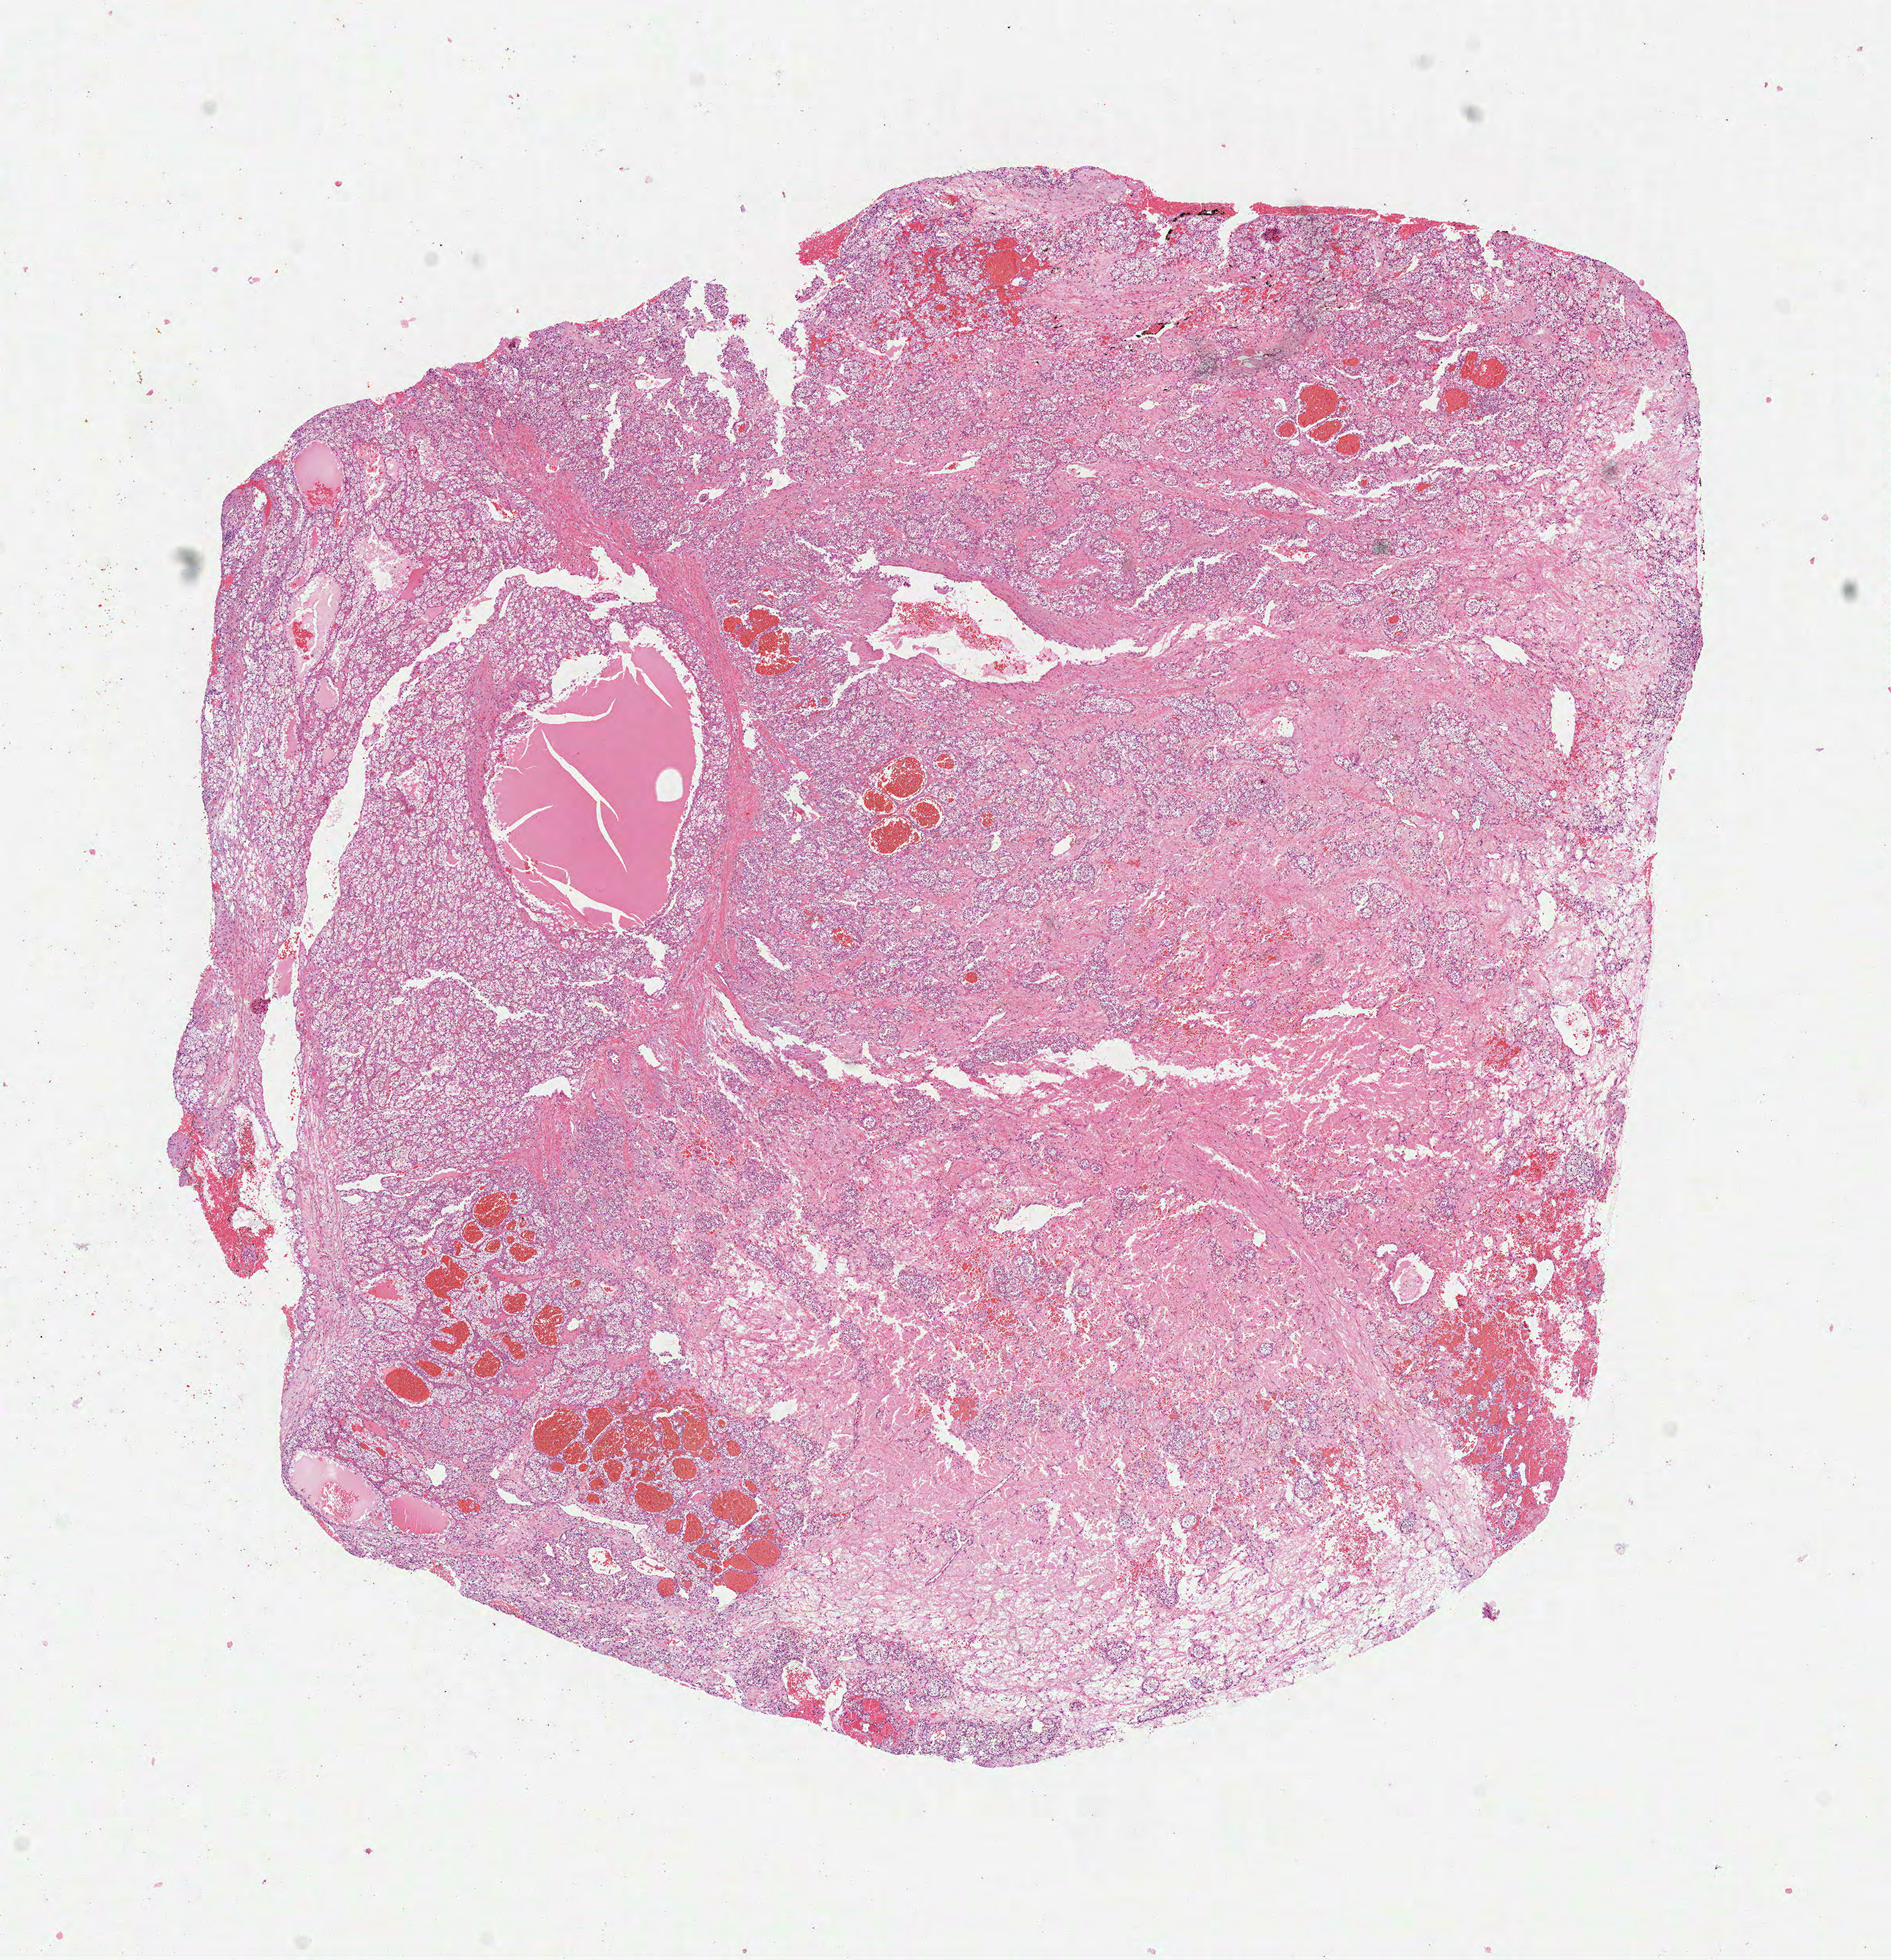
Digitized H&E-stained tissue section (whole slide) — a low-resolution overview of the entire scanned area, about 9.7 x 10.0 mm; FFPE section; kidney, primary tumour sample. Female patient; age at initial diagnosis 54 years. Histologic grade: G3 (poorly differentiated).
Pathologic diagnosis: Clear cell adenocarcinoma, NOS. AJCC pathologic stage: I.